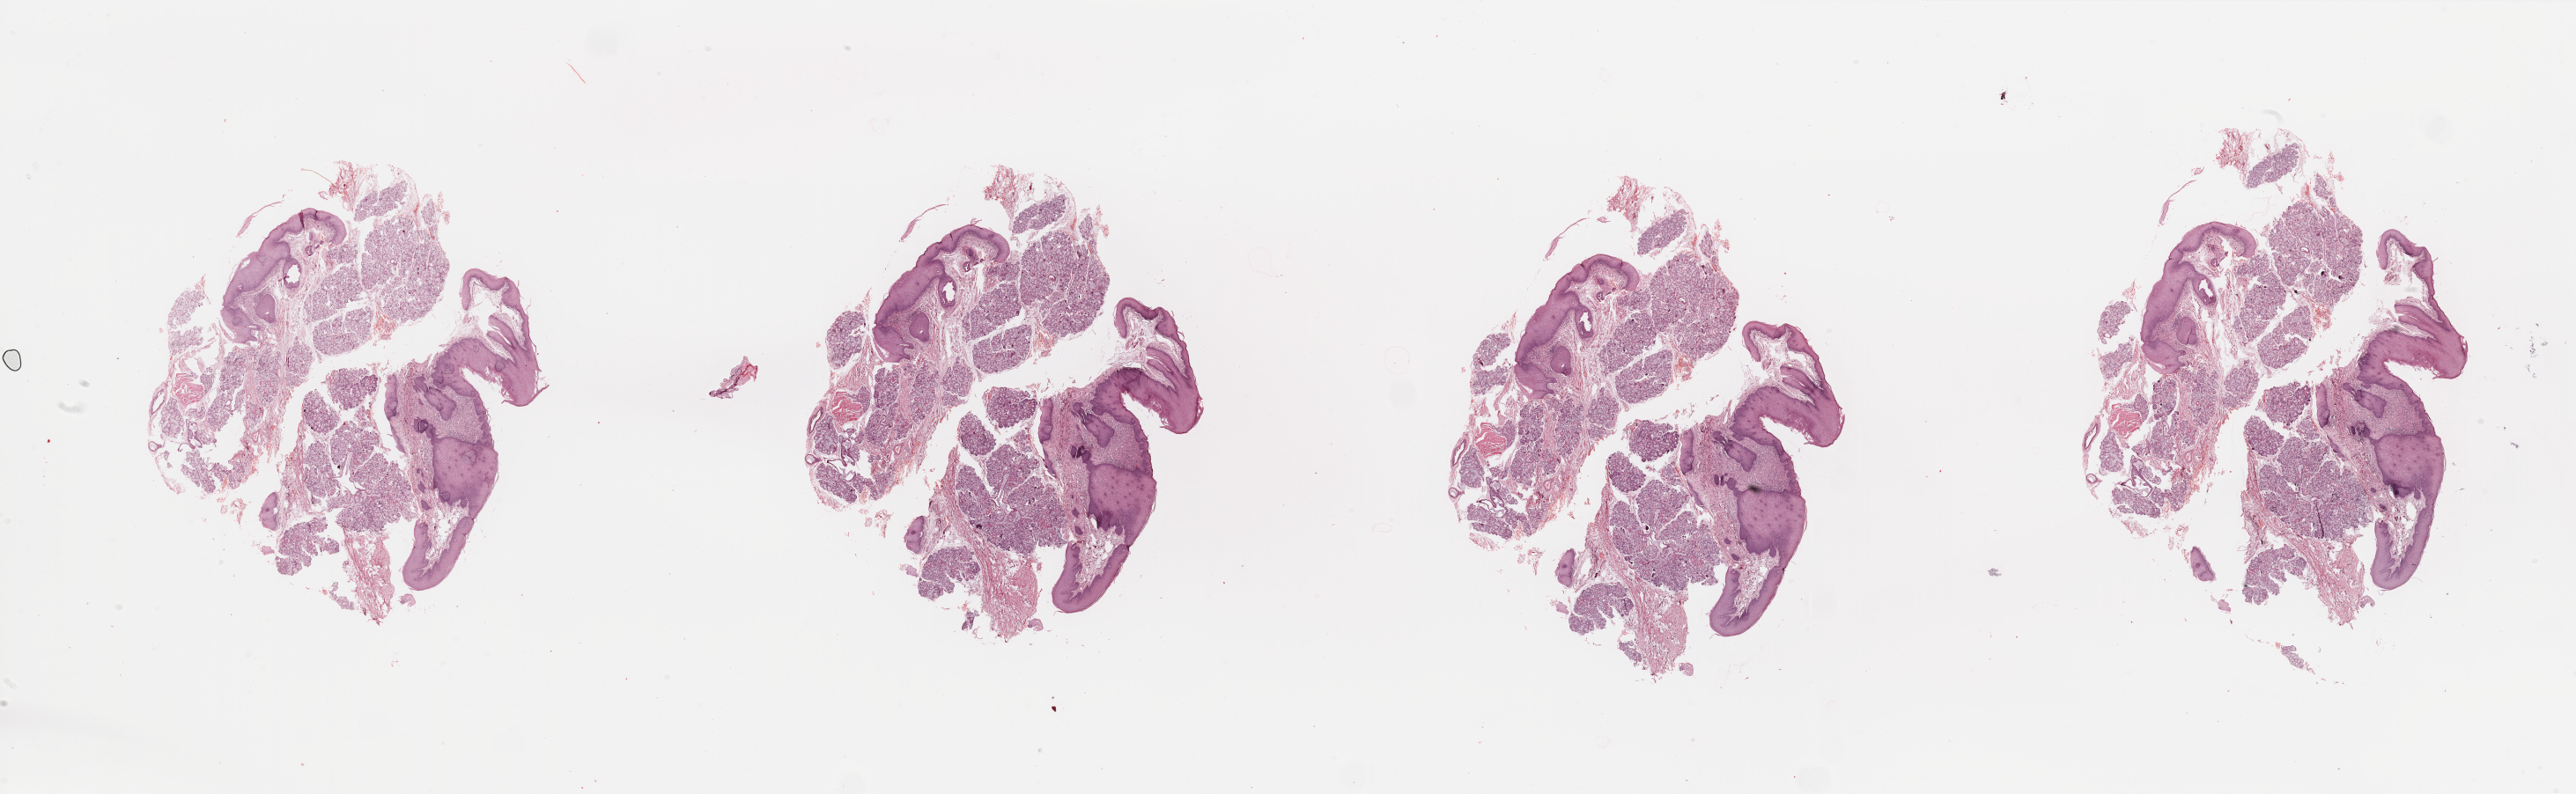
Whole-slide histology image, H&E-stained — a low-resolution overview of the entire scanned area, about 46.3 x 14.3 mm (from a 20x scan), normal (non-tumour) tissue sample, sampled site: larynx. Male, 81 y/o.
This section: normal (non-tumour) tissue from the same patient. Patient diagnosis: Squamous cell carcinoma, NOS.